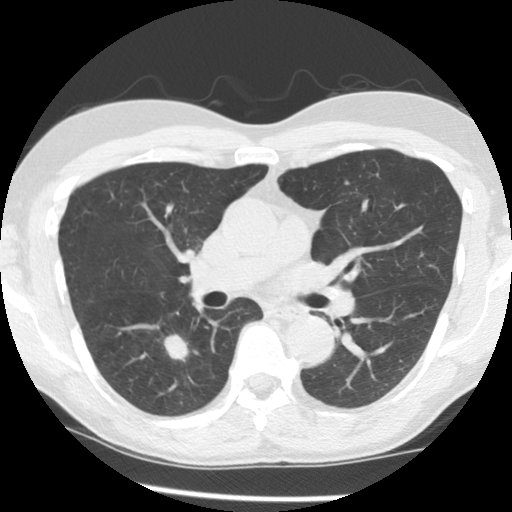
Low-dose screening chest CT, one axial slice; slice 81 of 145 in the series (ordered by position); reconstruction kernel STANDARD; 140 kVp; lung window (W 1500 / L -600 HU); 2.5 mm slice thickness; 512 × 512 image matrix.
Outlined on this slice (manually delineated by an expert):
- lesion 1 (tumor, lower lobe of right lung): box from (x=164, y=334) to (x=189, y=361) px